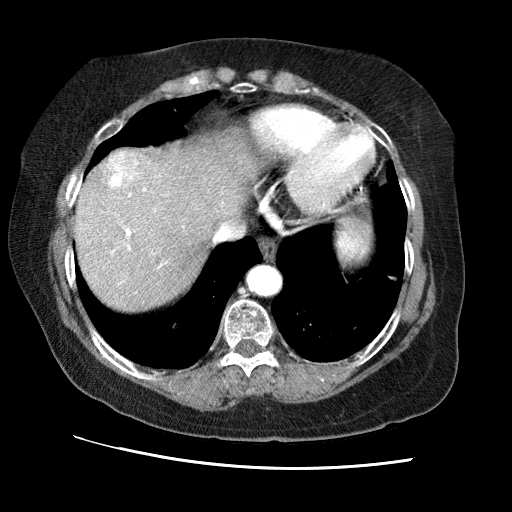
Contrast-enhanced abdominal CT (liver protocol), one axial slice. Slice 59 of 65 in the series (ordered by position). Reconstruction kernel STANDARD. 120 kVp. Soft-tissue window (W 400 / L 40 HU). 2.5 mm slice thickness. 512 × 512 image matrix, field of view 340 × 340 mm. From the clinical record (not read from this slice): diagnosis: hepatocellular carcinoma (patient treated with transarterial chemoembolisation; whether this scan precedes or follows treatment is not stated here); TNM stage (as recorded): Stage-II; Child-Pugh class: A; tumour differentiation: no biopsy; tumour nodularity: multinodular.
Structures marked on this image (semi-automatically segmented with operator editing):
- abdominal aorta: bounding box [x1, y1, x2, y2] px = [249, 266, 280, 295]
- liver parenchyma outside the tumour (the mass and vessels are separate outlines, so this box may not span the whole liver): [74, 134, 256, 310]
- mass: [107, 149, 145, 187]
- liver vessels: [110, 183, 163, 268]